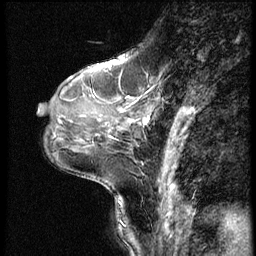
Breast MRI (dynamic contrast-enhanced), one sagittal slice; slice 24 of 62 in the series (ordered by position); dynamic contrast-enhanced series, image 2 of 4 at this slice position (ordered by acquisition); 1.5 T; TE 4.2 ms, TR 9 ms; 2.5 mm slice thickness; 256 × 256 image matrix. Female patient, age 46 years. From the clinical record (not read from this slice): setting: breast cancer imaged before/during neoadjuvant chemotherapy; receptor status: HER2-positive.
Outlined on this slice (semi-automatic segmentation, software-assisted and operator-edited):
- analysis volume of interest (the breast-tissue region the enhancement analysis was run in; not a lesion): box from (x=84, y=80) to (x=176, y=140) px
- tumour enhancement mask (voxels above the 140 % enhancement threshold inside the analysis volume of interest): (x=143, y=120)–(x=148, y=124)